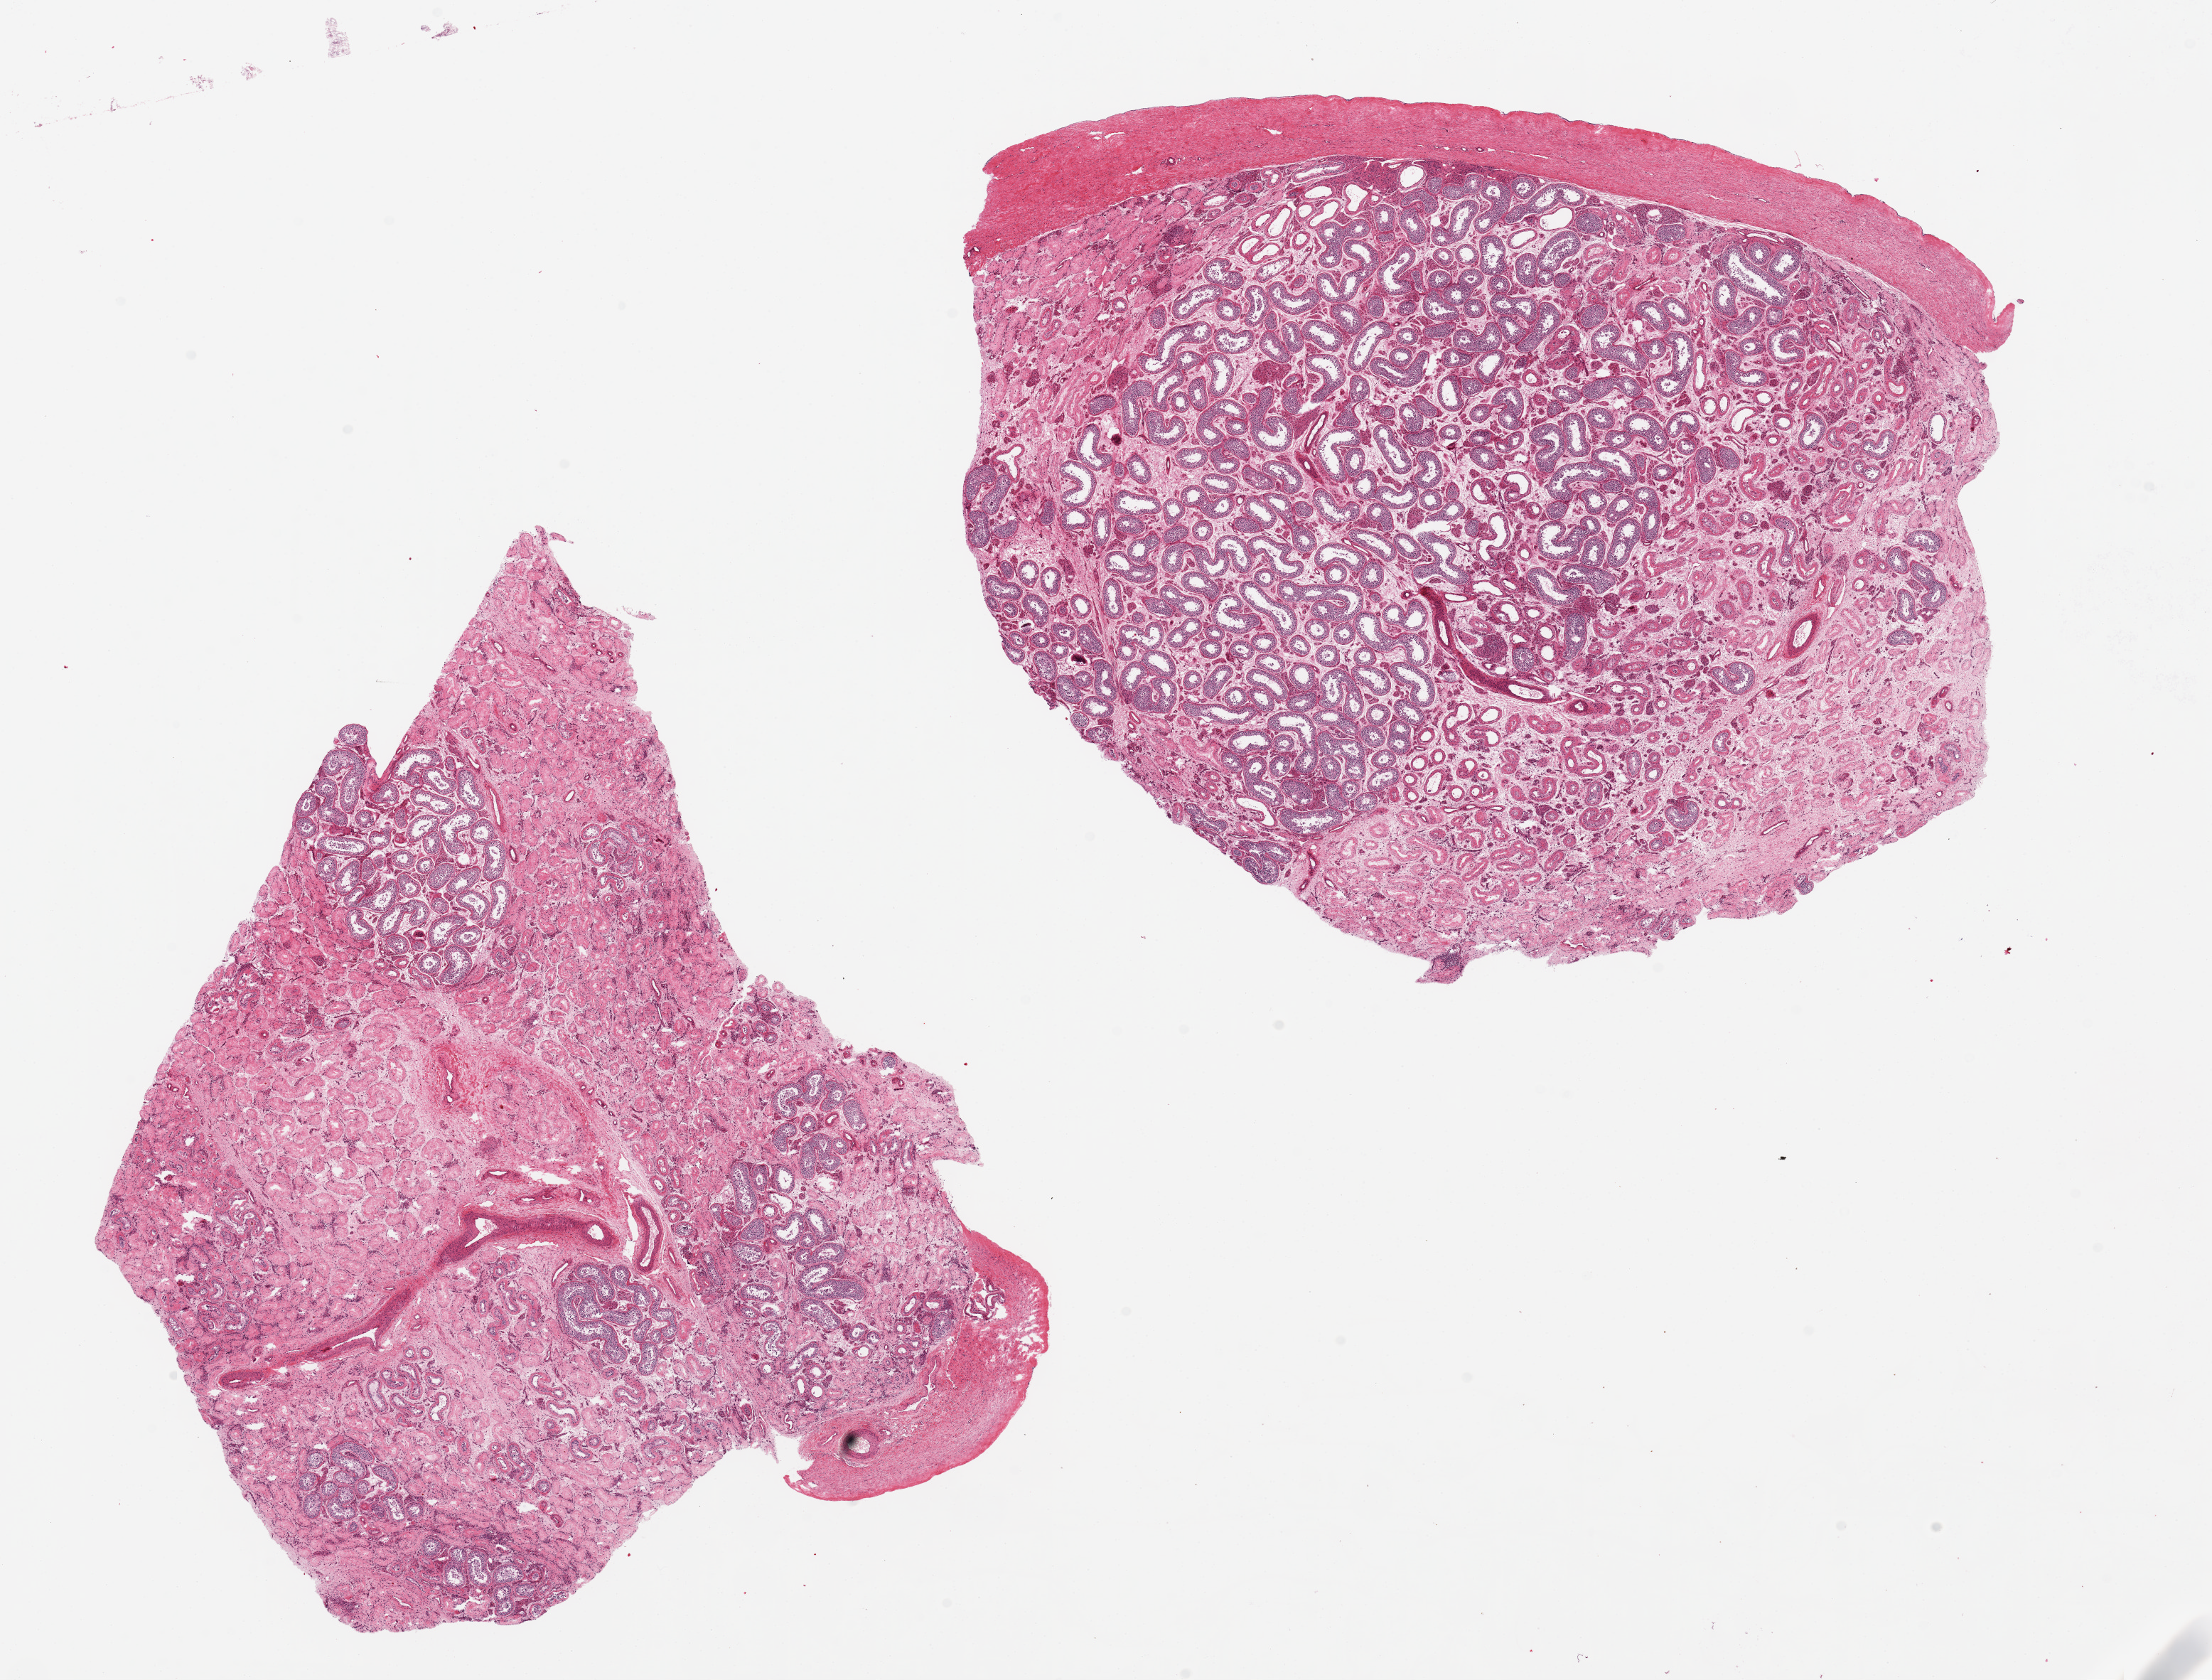
Digitized hematoxylin and eosin (H&E)-stained section — whole scanned area (about 24.6 x 18.7 mm) shown as a low-resolution overview. PAXgene-fixed, paraffin-embedded tissue. Target tissue: testis. Tissue donor sample. Male donor.
Reviewer comment on this tissue sample: 2 pieces ~10mm sq; >60% atrophic, sclerotic tubules; remainder with minimal spermatogenesis. Capsule partially present.